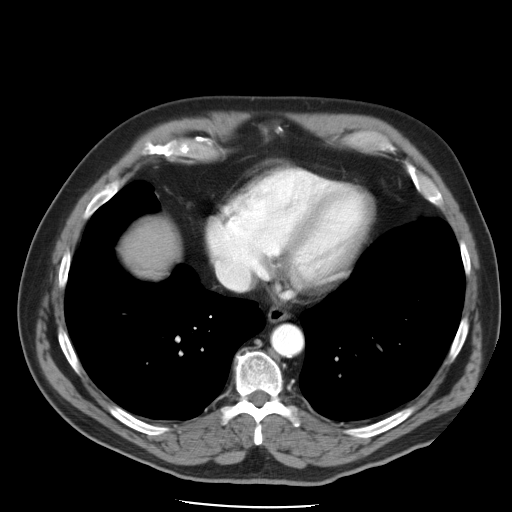
Contrast-enhanced abdominal CT, one axial slice. Position 46 of 49 along the scan axis. Reconstruction kernel STANDARD. 120 kVp. Intravenous contrast given. Soft-tissue window (W 400 / L 40 HU). 512 × 512 image matrix, field of view 395 × 395 mm. Male patient, age 68 years. From the clinical record (not read from this slice): diagnosis: colorectal cancer liver metastases, imaged before liver resection; multiple liver metastases: yes; largest metastasis: 1.7 cm; disease in both lobes: no.
Outlined on this slice (manually delineated by an expert):
- hepatic veins: bounding box [x1, y1, x2, y2] px = [215, 256, 254, 290]
- liver: [129, 222, 173, 267]
- planned liver remnant (the part of the liver to remain after resection): [129, 222, 174, 267]